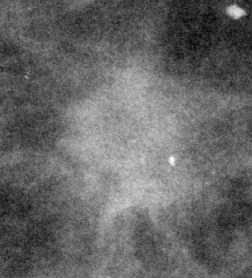
Cropped region of a digitized screen-film mammogram centred on a radiologist-marked abnormality, left breast, CC view.
- Finding: mass, shape irregular, margins spiculated; BI-RADS assessment category 4; pathology result (as recorded, not read from the image): malignant.